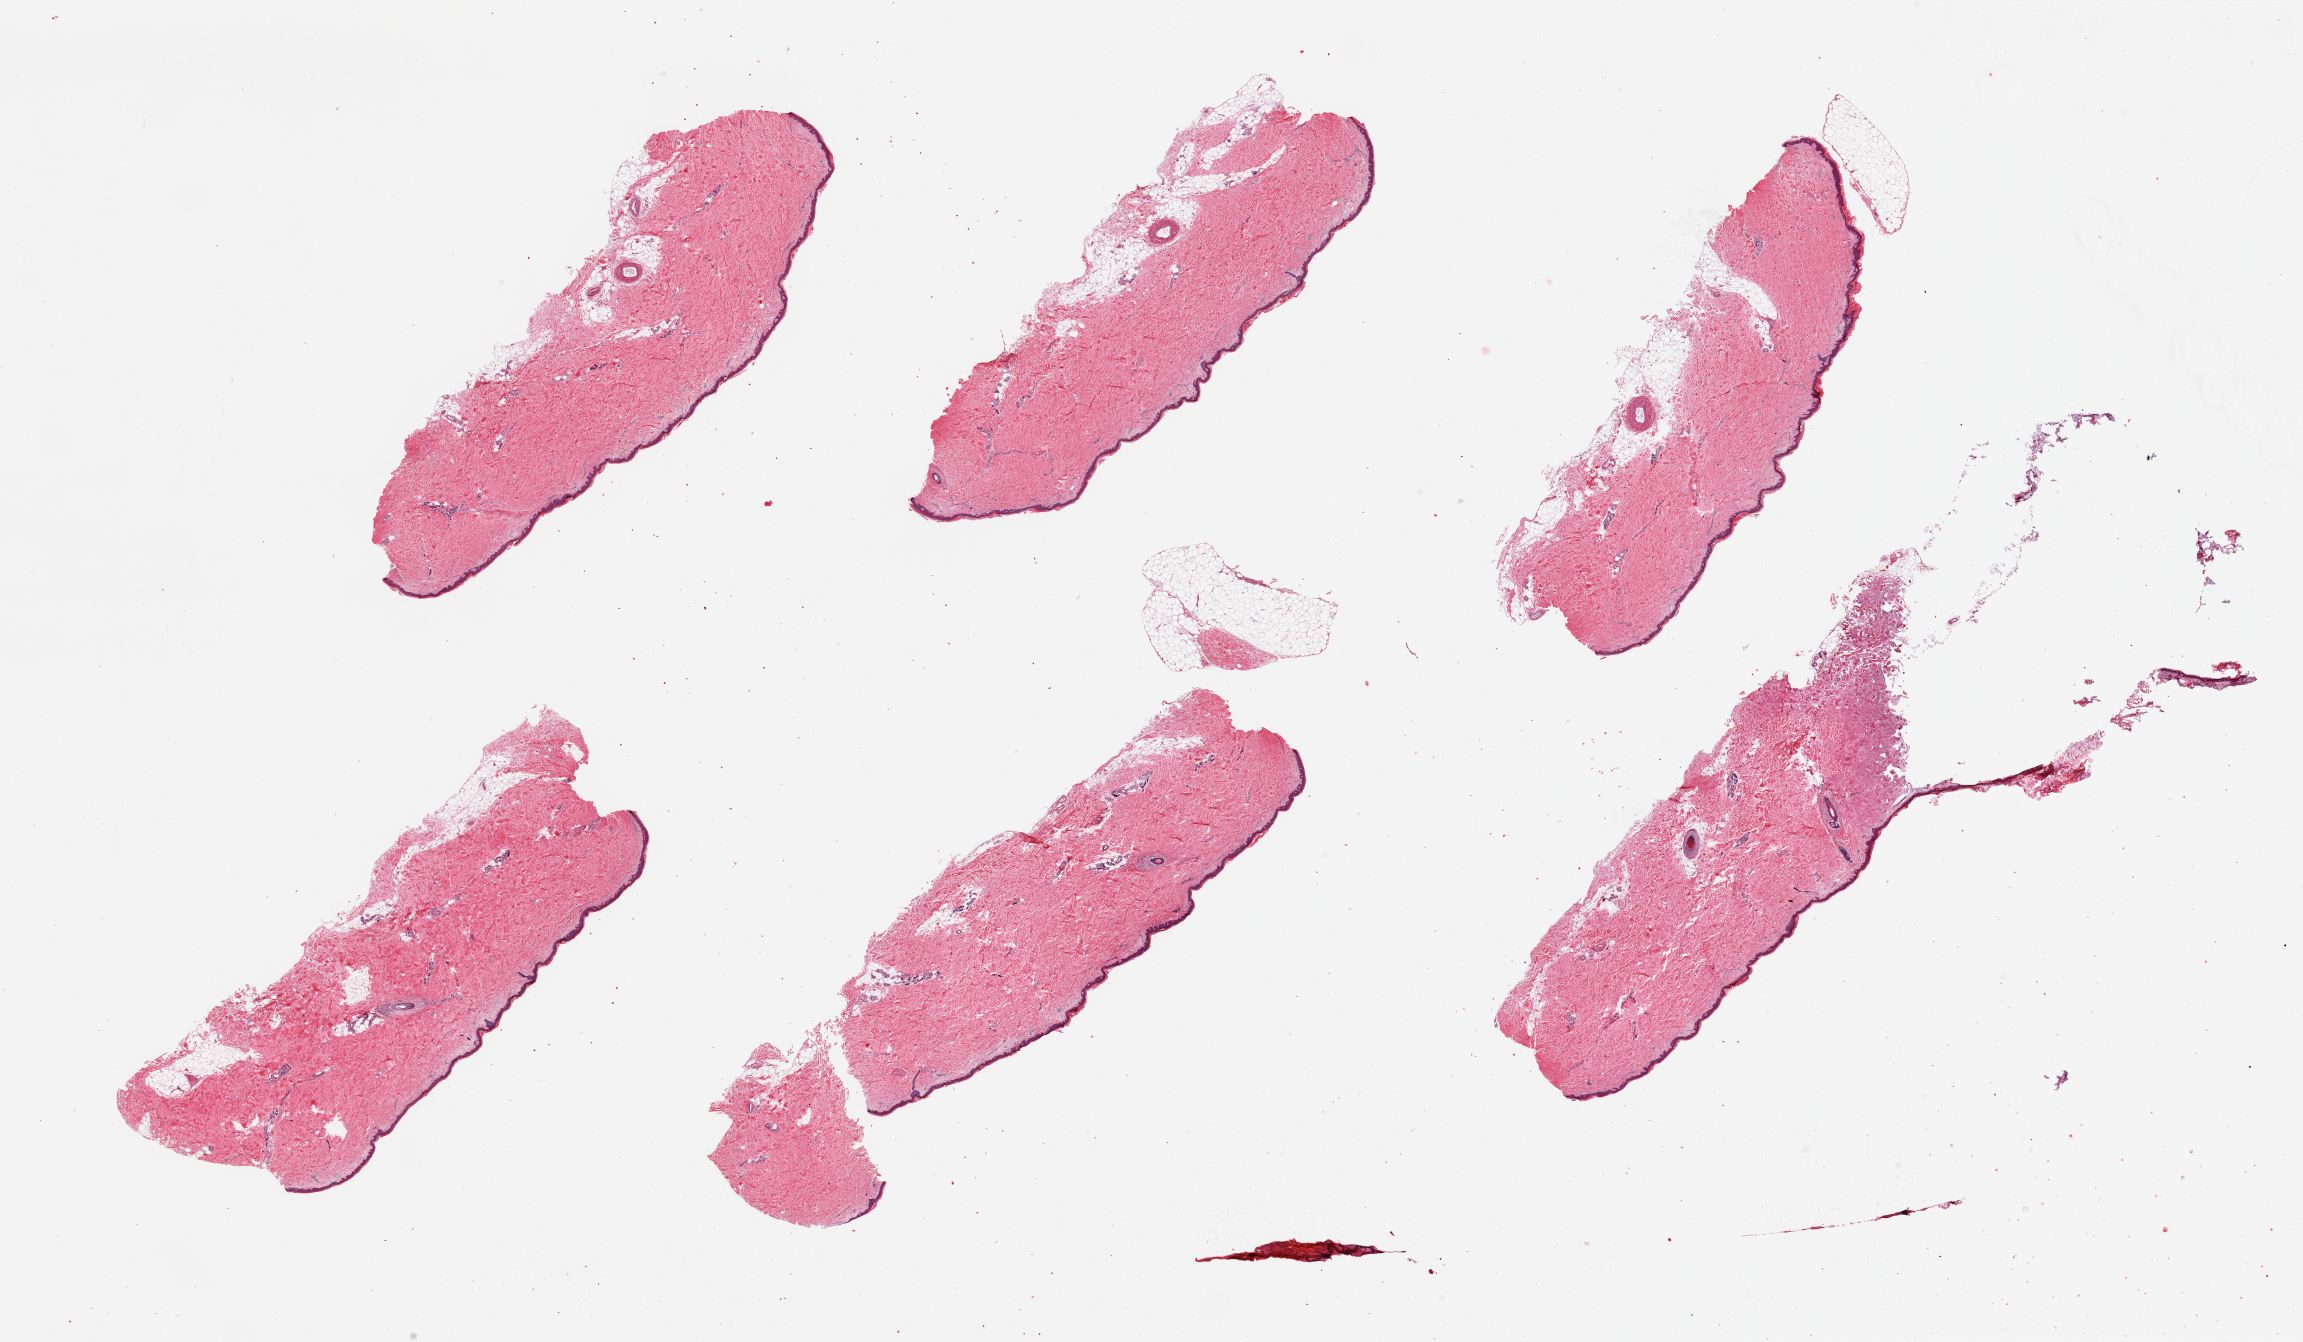
H&E whole-slide image, brightfield — shown as a low-resolution overview of the whole scanned area (about 36.4 x 21.2 mm, acquisition: 20x scan); PAXgene-fixed, paraffin-embedded tissue; sampled site (target tissue): skin of lower leg; tissue donor sample. Donor: male.
Reviewer comment on this tissue sample: 6 pieces. Well trimmed.